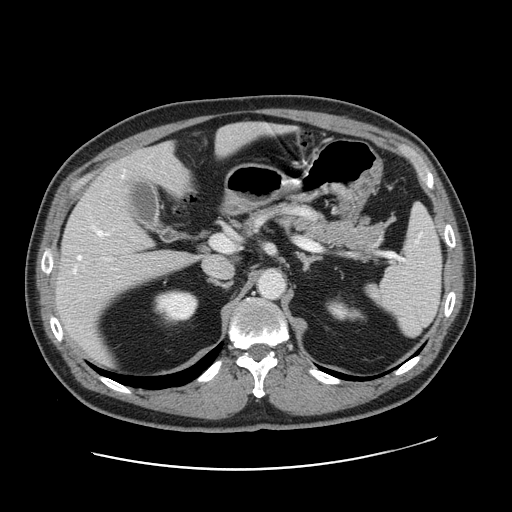
Contrast-enhanced abdominal CT, one axial slice. 120 kVp. Intravenous contrast given. Soft-tissue window (W 400 / L 40 HU). 2.5 mm slice thickness. 512 × 512 image matrix. Male patient, age 63 years. From the clinical record (not read from this slice): diagnosis: colorectal cancer liver metastases, imaged before liver resection; multiple liver metastases: yes; largest metastasis: 8 cm; chemotherapy before resection: no.
Structures marked on this image (outlined manually by an expert reader):
- hepatic veins: box from (x=74, y=175) to (x=124, y=273) px
- liver: (x=56, y=123)–(x=280, y=361)
- planned liver remnant (the part of the liver to remain after resection): (x=119, y=123)–(x=281, y=195)
- portal vein (with intrahepatic branches): (x=105, y=235)–(x=233, y=260)